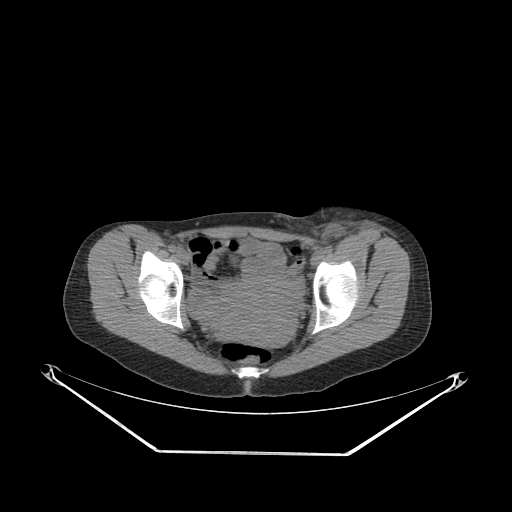
CT of an extremity soft-tissue mass (from a PET/CT study), one axial slice; position 76 of 267 along the scan axis; reconstruction kernel SOFT; soft-tissue window (W 400 / L 40 HU); 3.75 mm slice thickness; 512 × 512 image matrix, field of view 500 × 500 mm. Female patient. From the clinical record (not read from this slice): histological type: leiomyosarcoma; grade: high; site of the primary tumour: groin.
Outlined on this slice (expert contour drawn on MRI and transferred to this co-registered scan by the dataset authors):
- gross tumour volume including surrounding oedema: bounding box [x1, y1, x2, y2] px = [290, 210, 396, 252]
- gross tumour volume (mass): [299, 215, 344, 252]